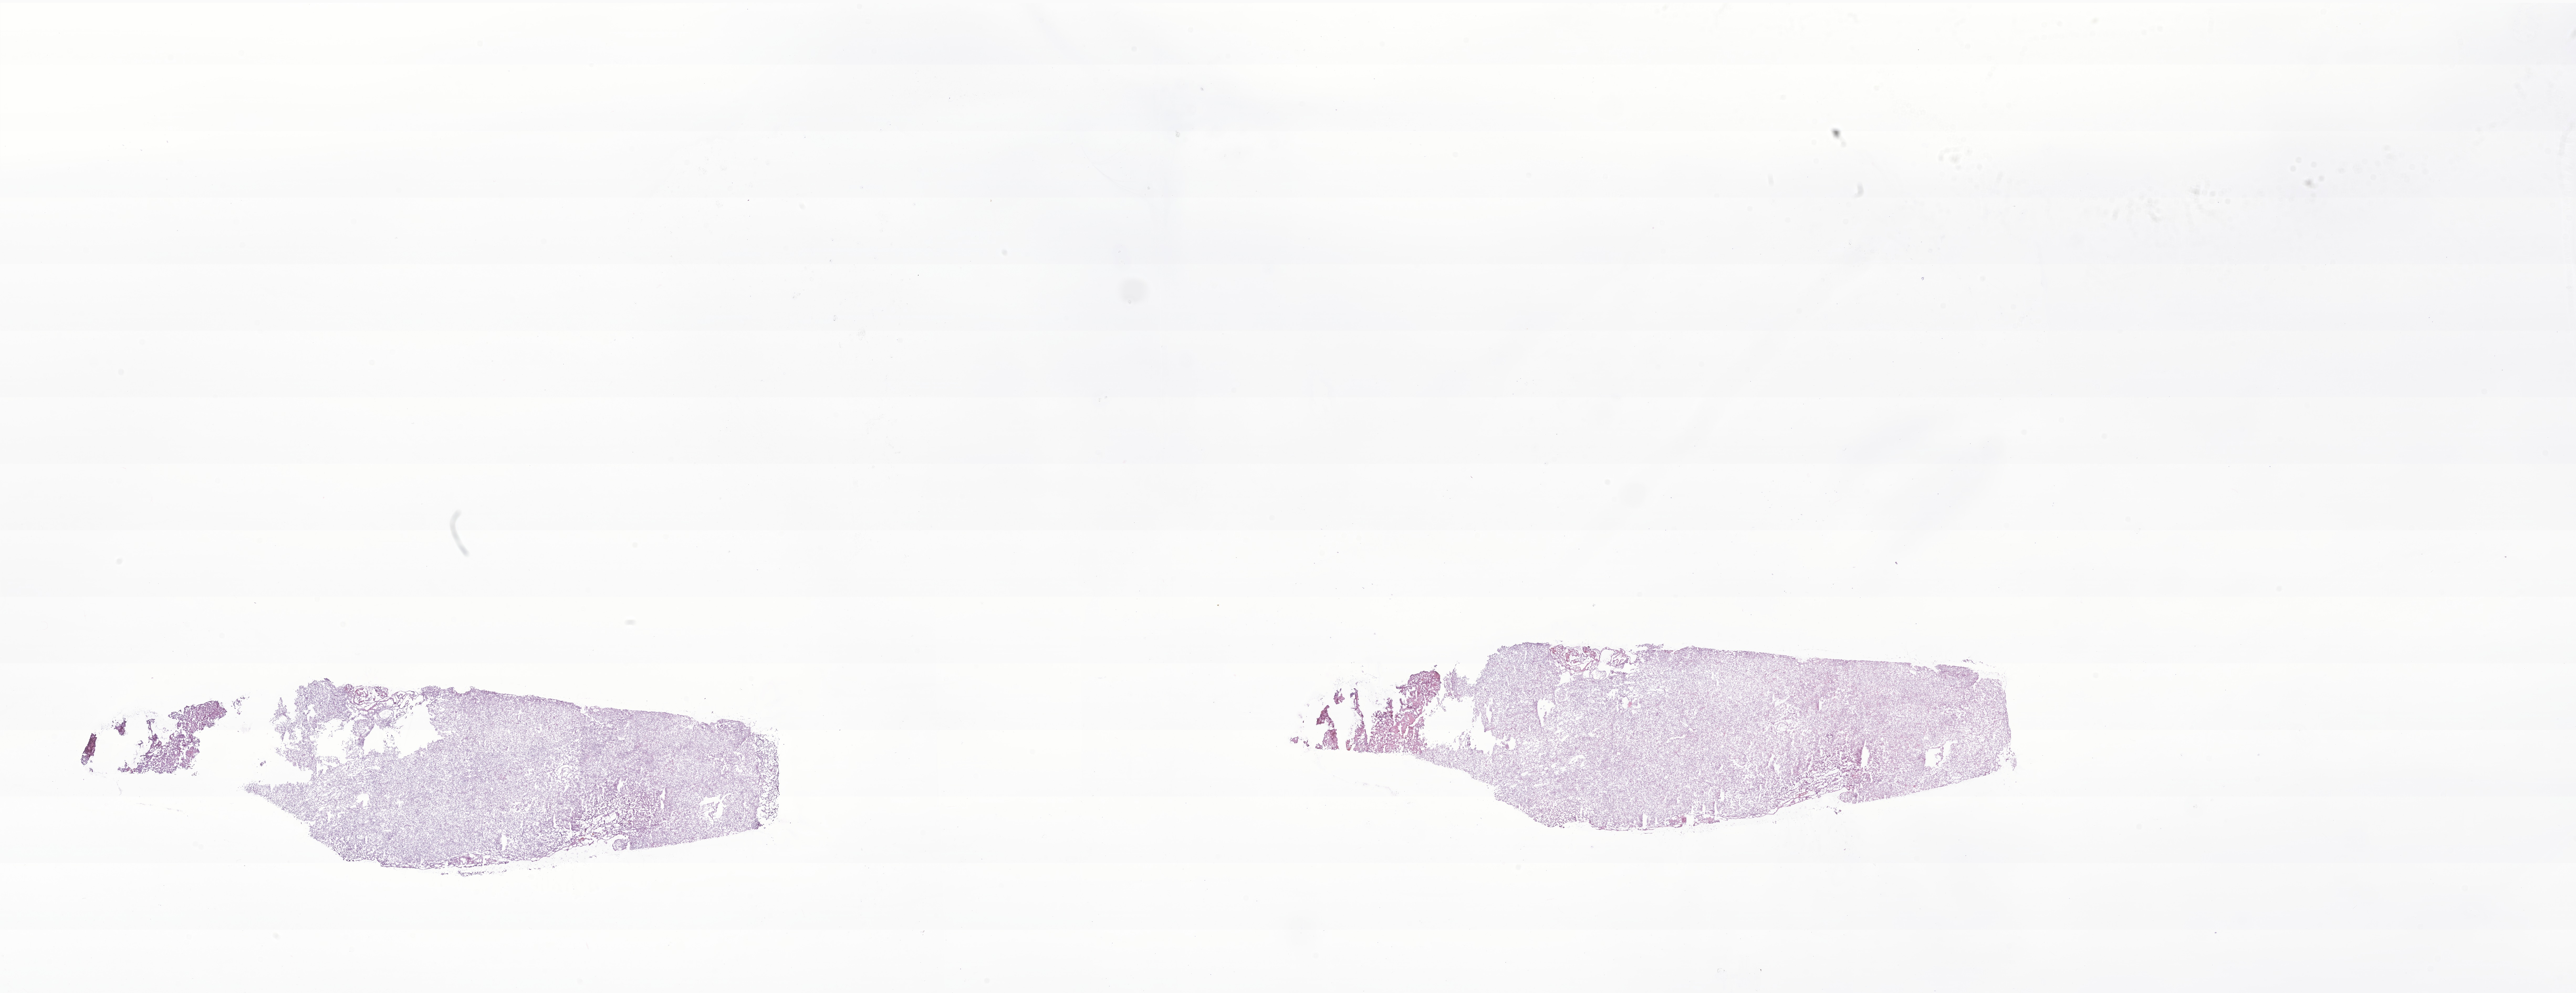
Digitized H&E-stained section of tumor tissue from the brain — a low-resolution overview of the entire scanned area, about 41.4 x 15.9 mm, frozen section (OCT-embedded). Patient: female, age 192 months (16 years).
Diagnosis (ICD-O-3 morphology term): Clear cell meningioma.